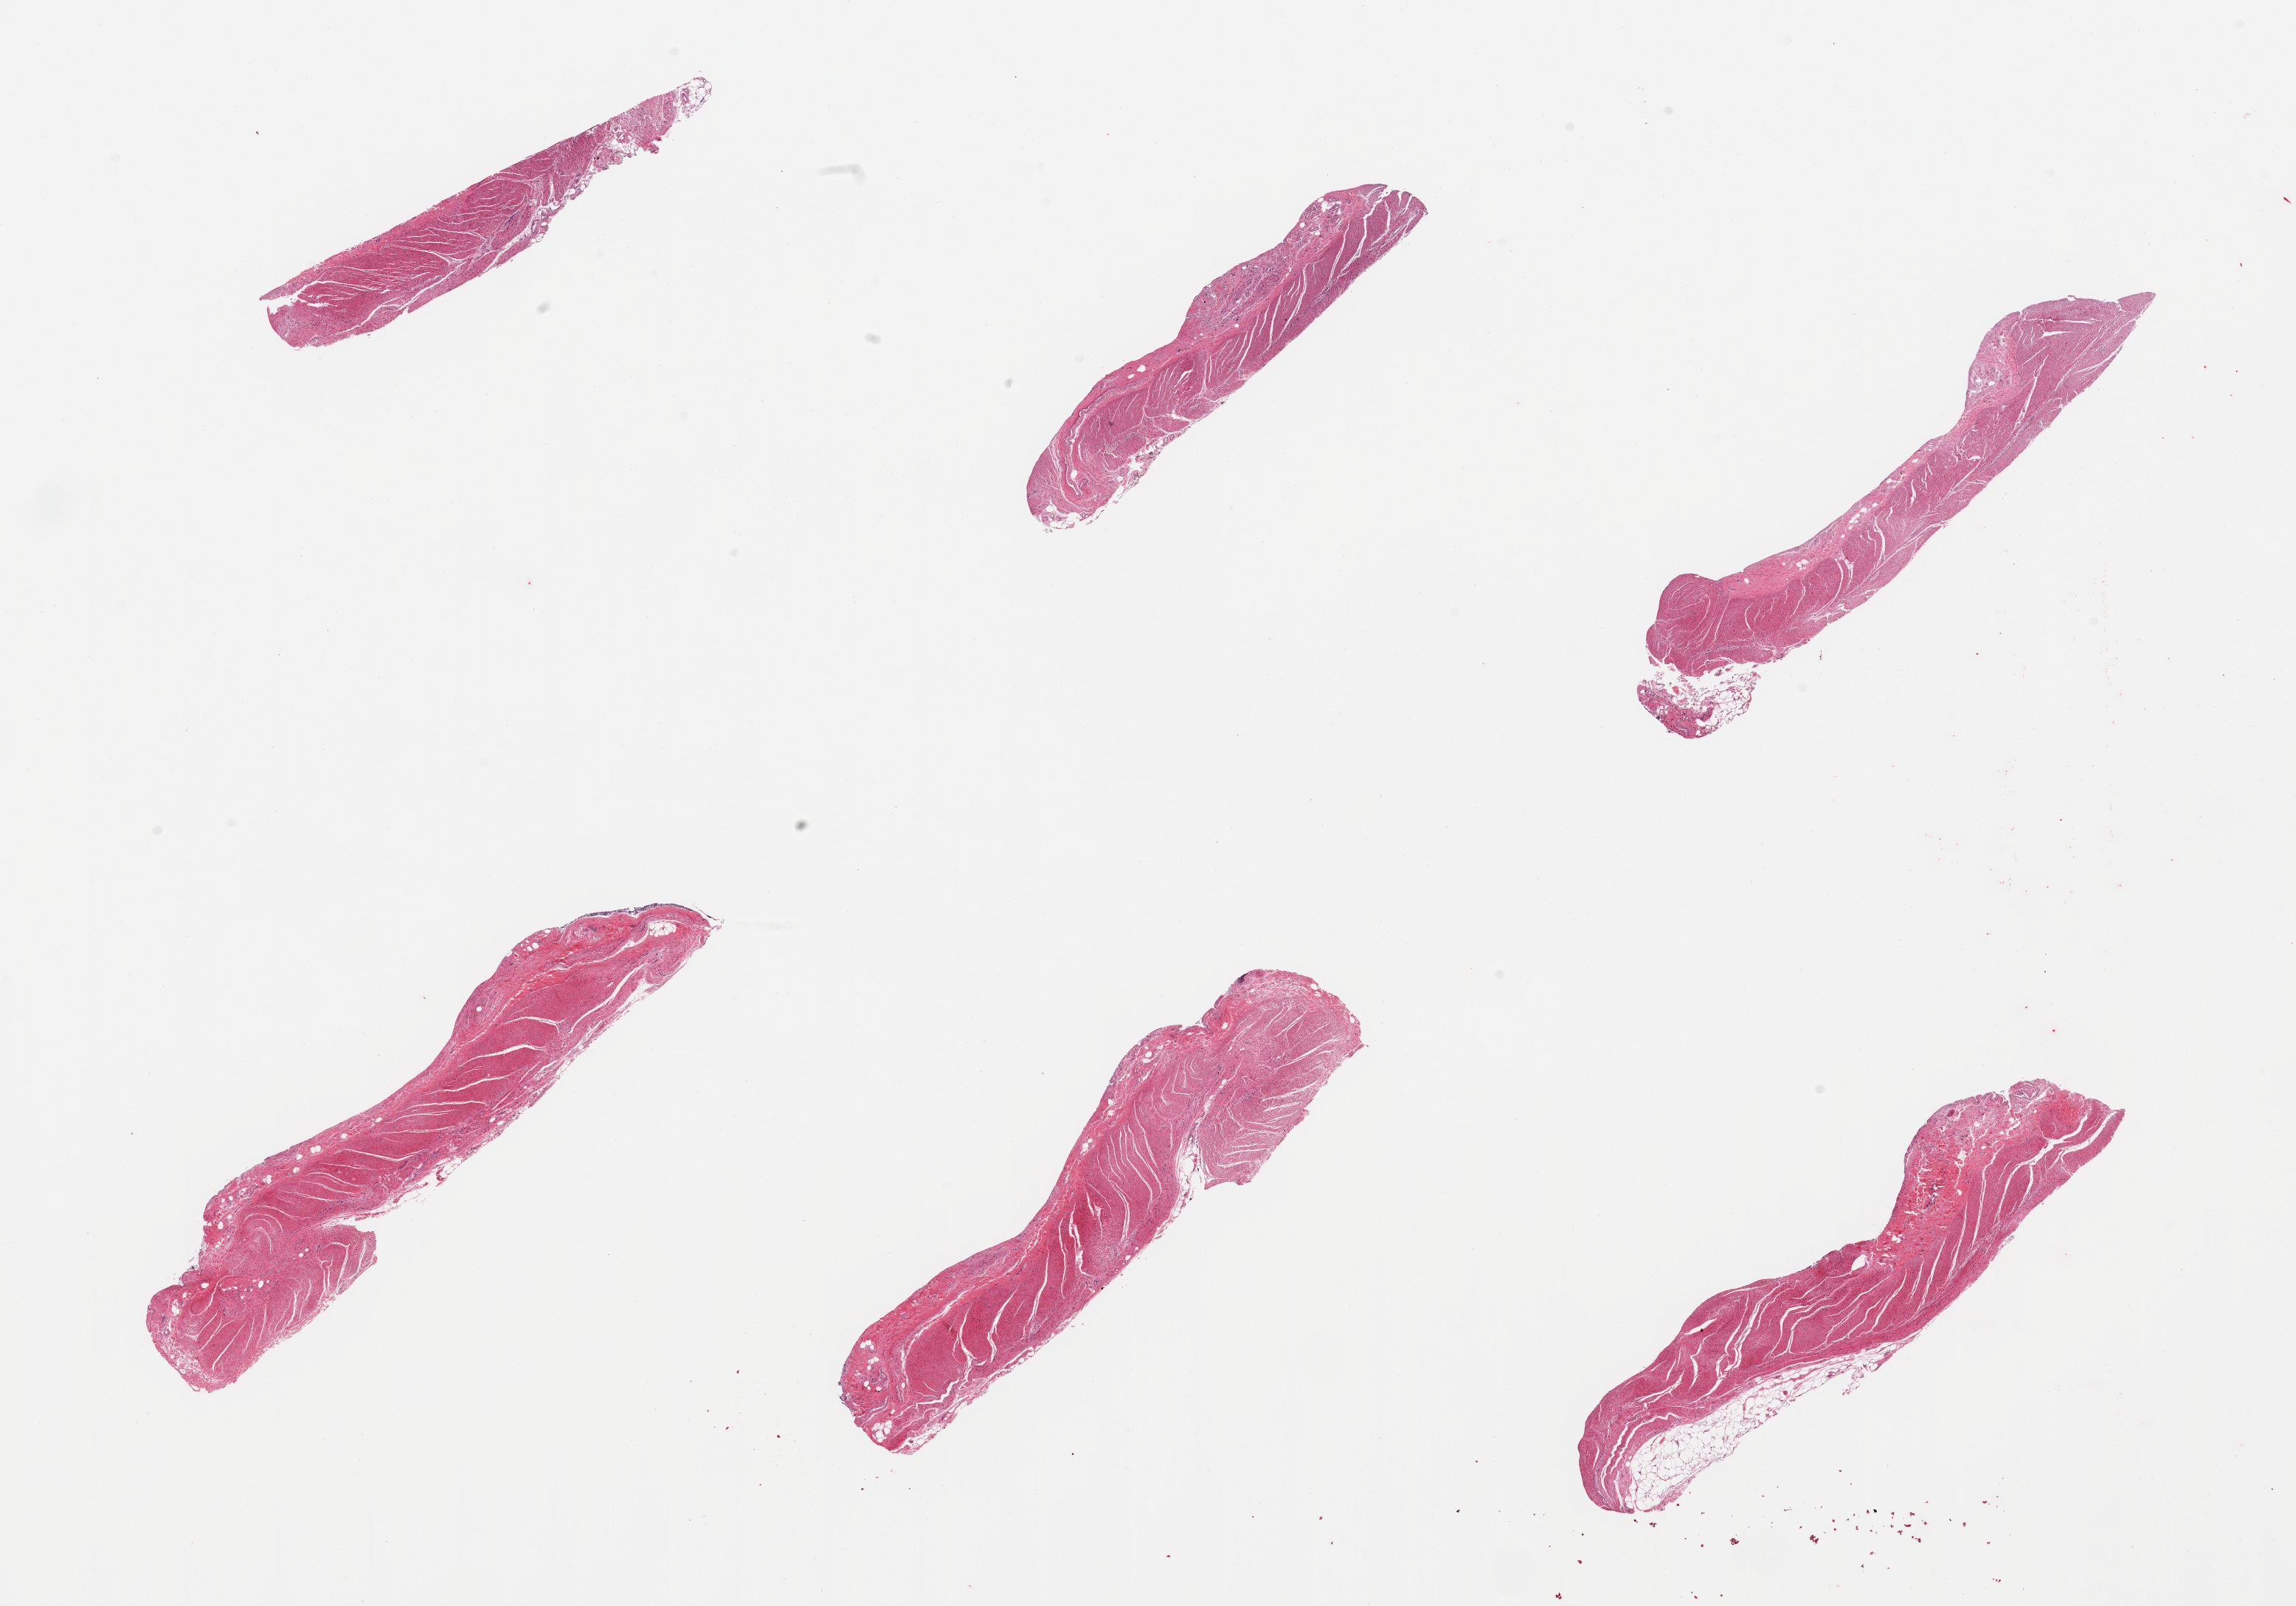
Digitized H&E-stained section — shown as a low-resolution overview of the whole scanned area (about 24.6 x 17.2 mm); PAXgene-fixed paraffin-embedded (PFPE) section; section of sigmoid colon (target tissue); donor tissue sample. Donor: male.
Review note (as recorded): 6 pieces.